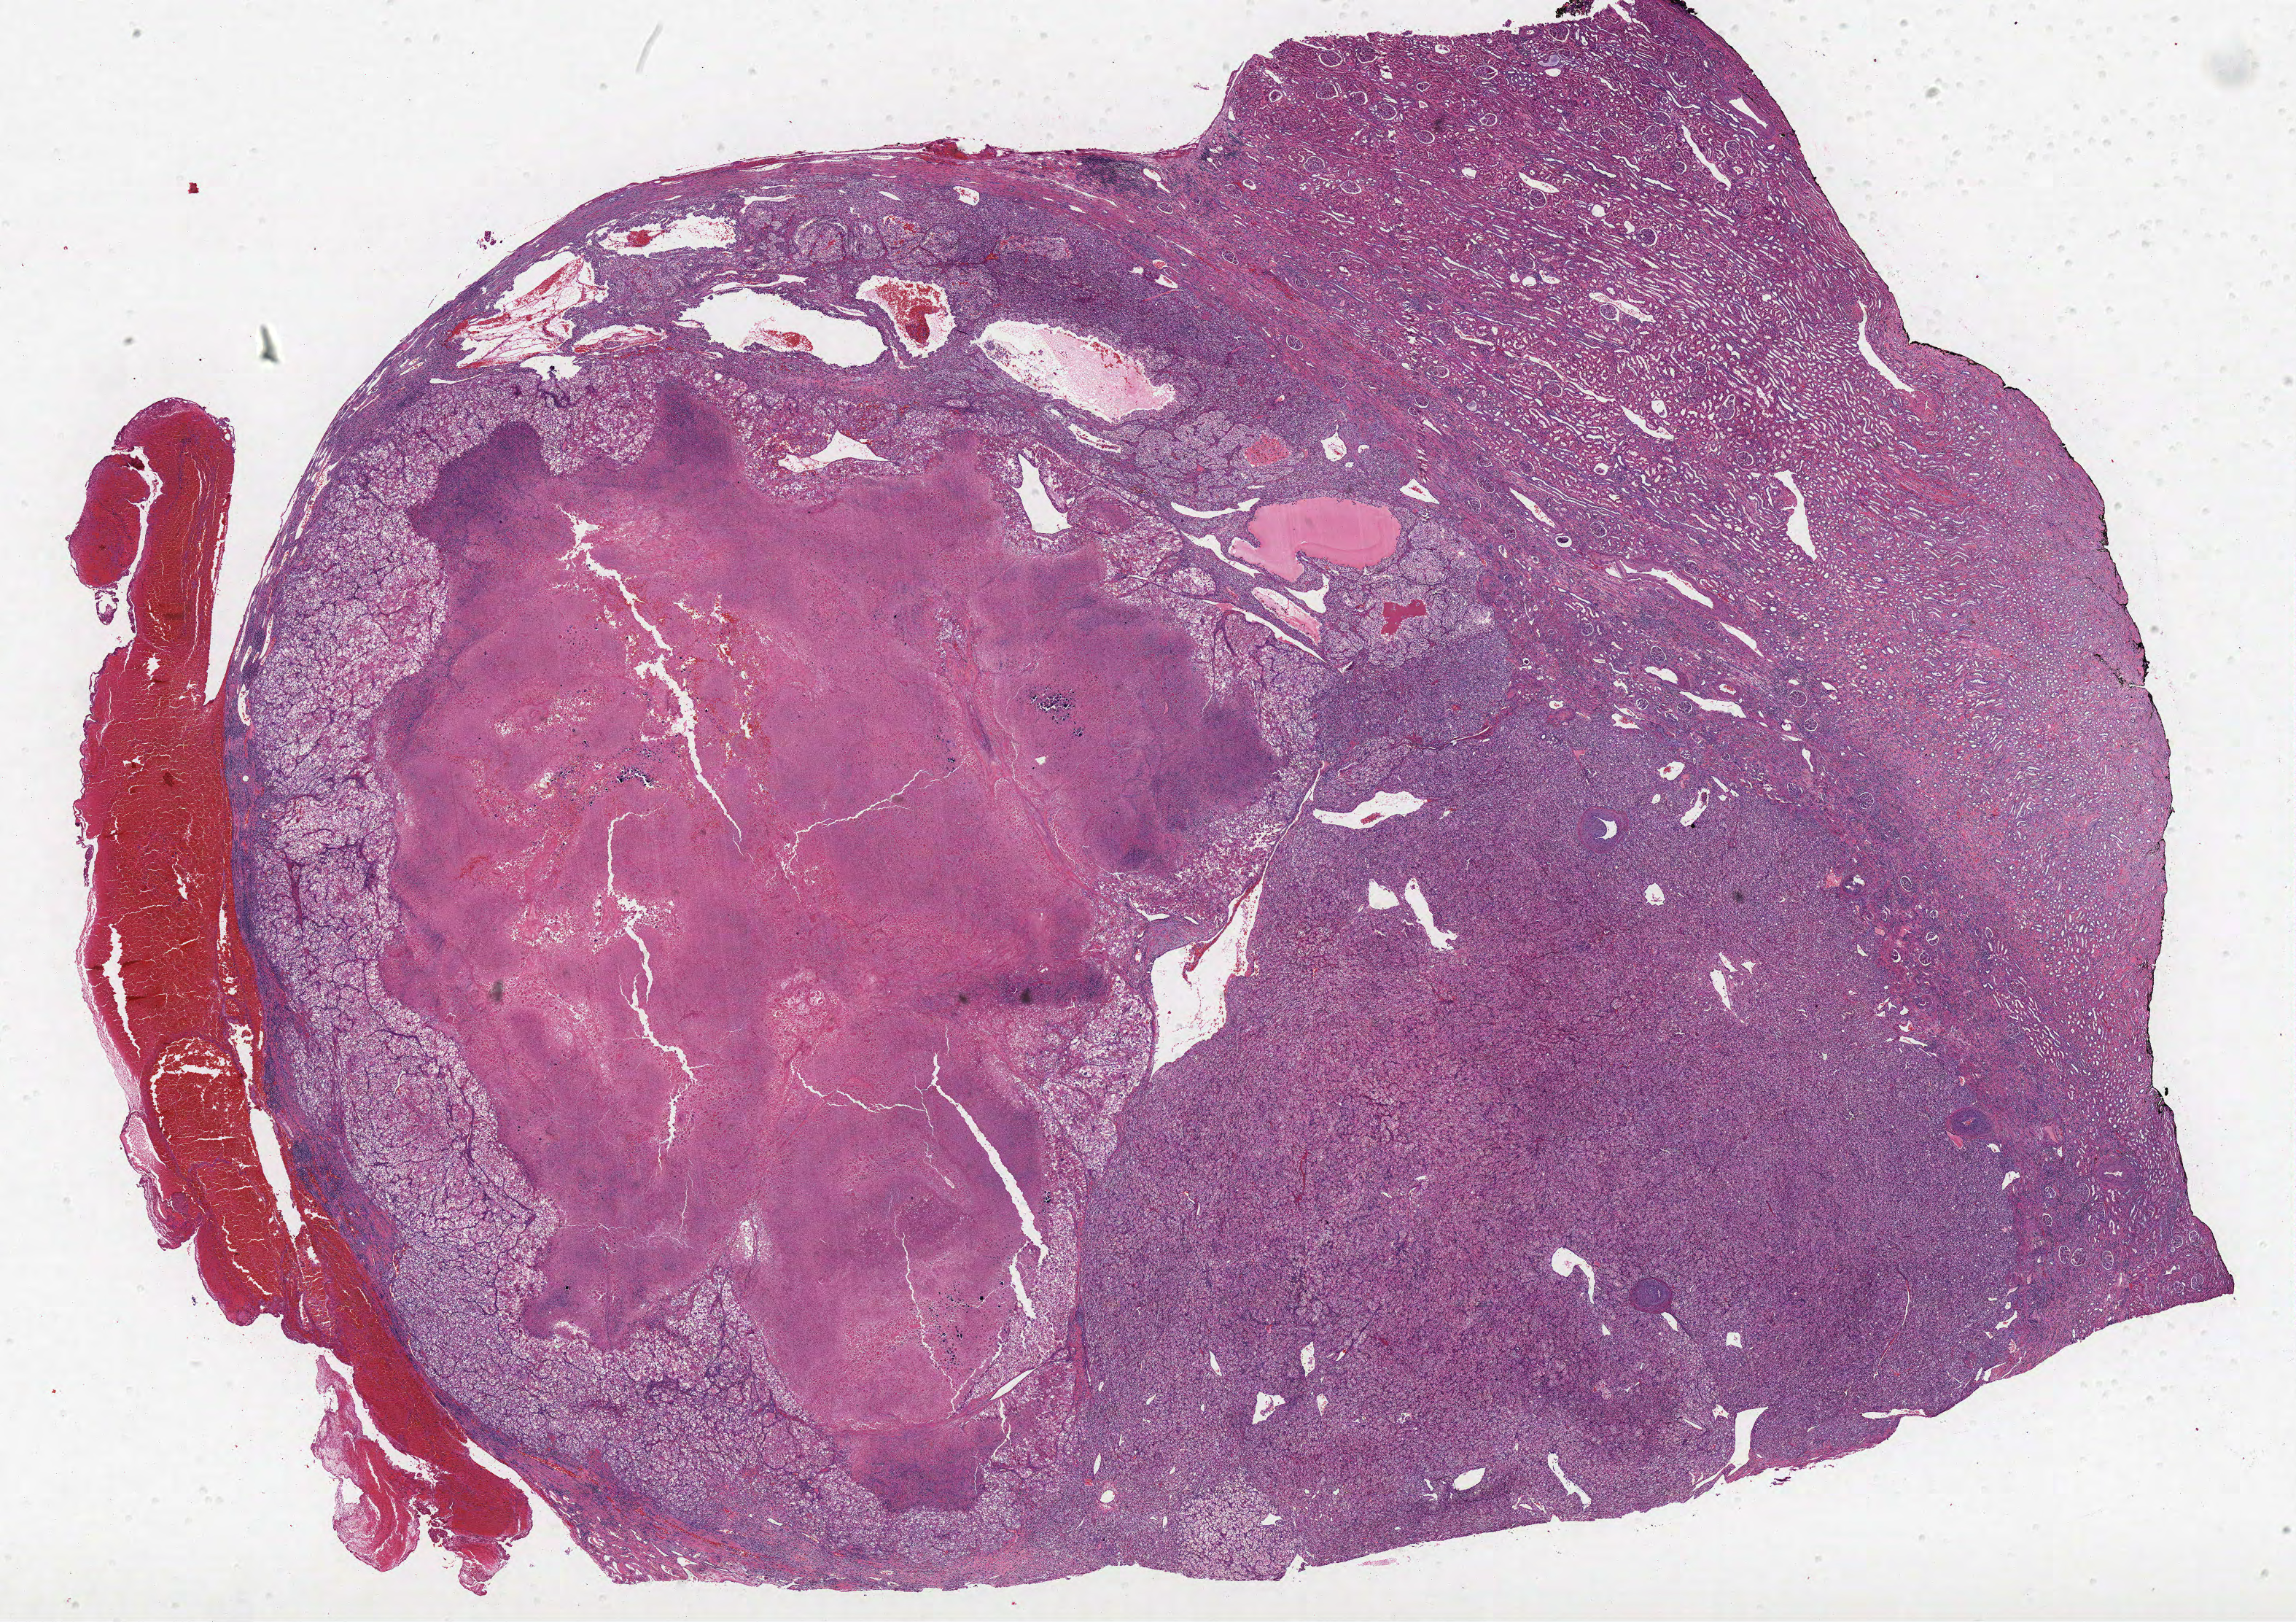
Digitized H&E-stained tissue section (whole slide) — shown as a low-resolution overview of the whole scanned area (about 25.2 x 17.8 mm), formalin-fixed paraffin-embedded (FFPE) diagnostic section, kidney, primary tumour sample. Patient: male, age at initial diagnosis 60 years. Histologic grade: G4 (undifferentiated).
Pathologic diagnosis: Clear cell adenocarcinoma, NOS. AJCC pathologic stage: I.